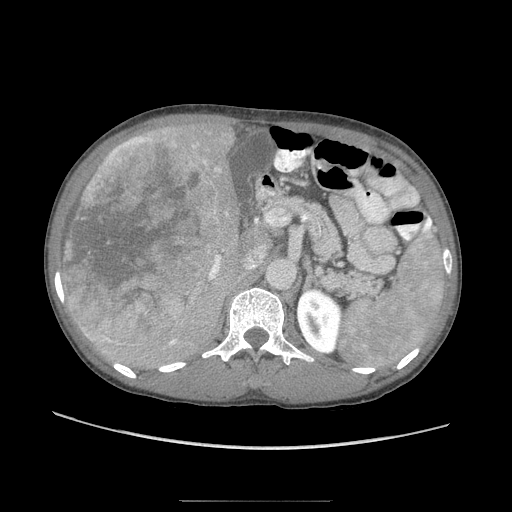
Contrast-enhanced abdominal CT (liver protocol), one axial slice; position 48 of 103 along the scan axis; reconstruction kernel STANDARD; 120 kVp; soft-tissue window (W 400 / L 40 HU); 2.5 mm slice thickness; 512 × 512 image matrix. Case-level facts recorded for this patient, not image findings: diagnosis: hepatocellular carcinoma (patient treated with transarterial chemoembolisation; whether this scan precedes or follows treatment is not stated here); TNM stage (as recorded): Stage-IIIA; Child-Pugh class: A.
Outlined on this slice (semi-automatically segmented with operator editing):
- liver parenchyma outside the tumour (the mass and vessels are separate outlines, so this box may not span the whole liver): bounding box <66,124,246,372> (left, top, right, bottom; pixels)
- mass: <61,126,220,347>
- liver vessels: <193,248,226,298>